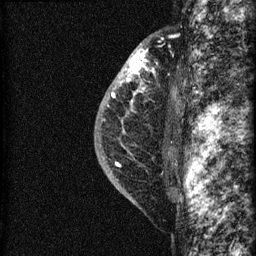
Breast MRI (dynamic contrast-enhanced), one sagittal slice; position 46 of 60 along the scan axis; dynamic contrast-enhanced series, image 2 of 3 at this slice position (ordered by acquisition); 1.5 T; TE 4.2 ms, TR 22.7 ms; 256 × 256 image matrix. Female patient, age 48 years. Case-level facts recorded for this patient, not image findings: setting: breast cancer imaged before/during neoadjuvant chemotherapy; receptor status: triple-negative.
Annotated regions visible in this slice (semi-automatic segmentation, software-assisted and operator-edited):
- analysis volume of interest (the breast-tissue region the enhancement analysis was run in; not a lesion): bounding box <115,34,169,162> (left, top, right, bottom; pixels)
- tumour enhancement mask (voxels above the 90 % enhancement threshold inside the analysis volume of interest): <126,51,147,104>